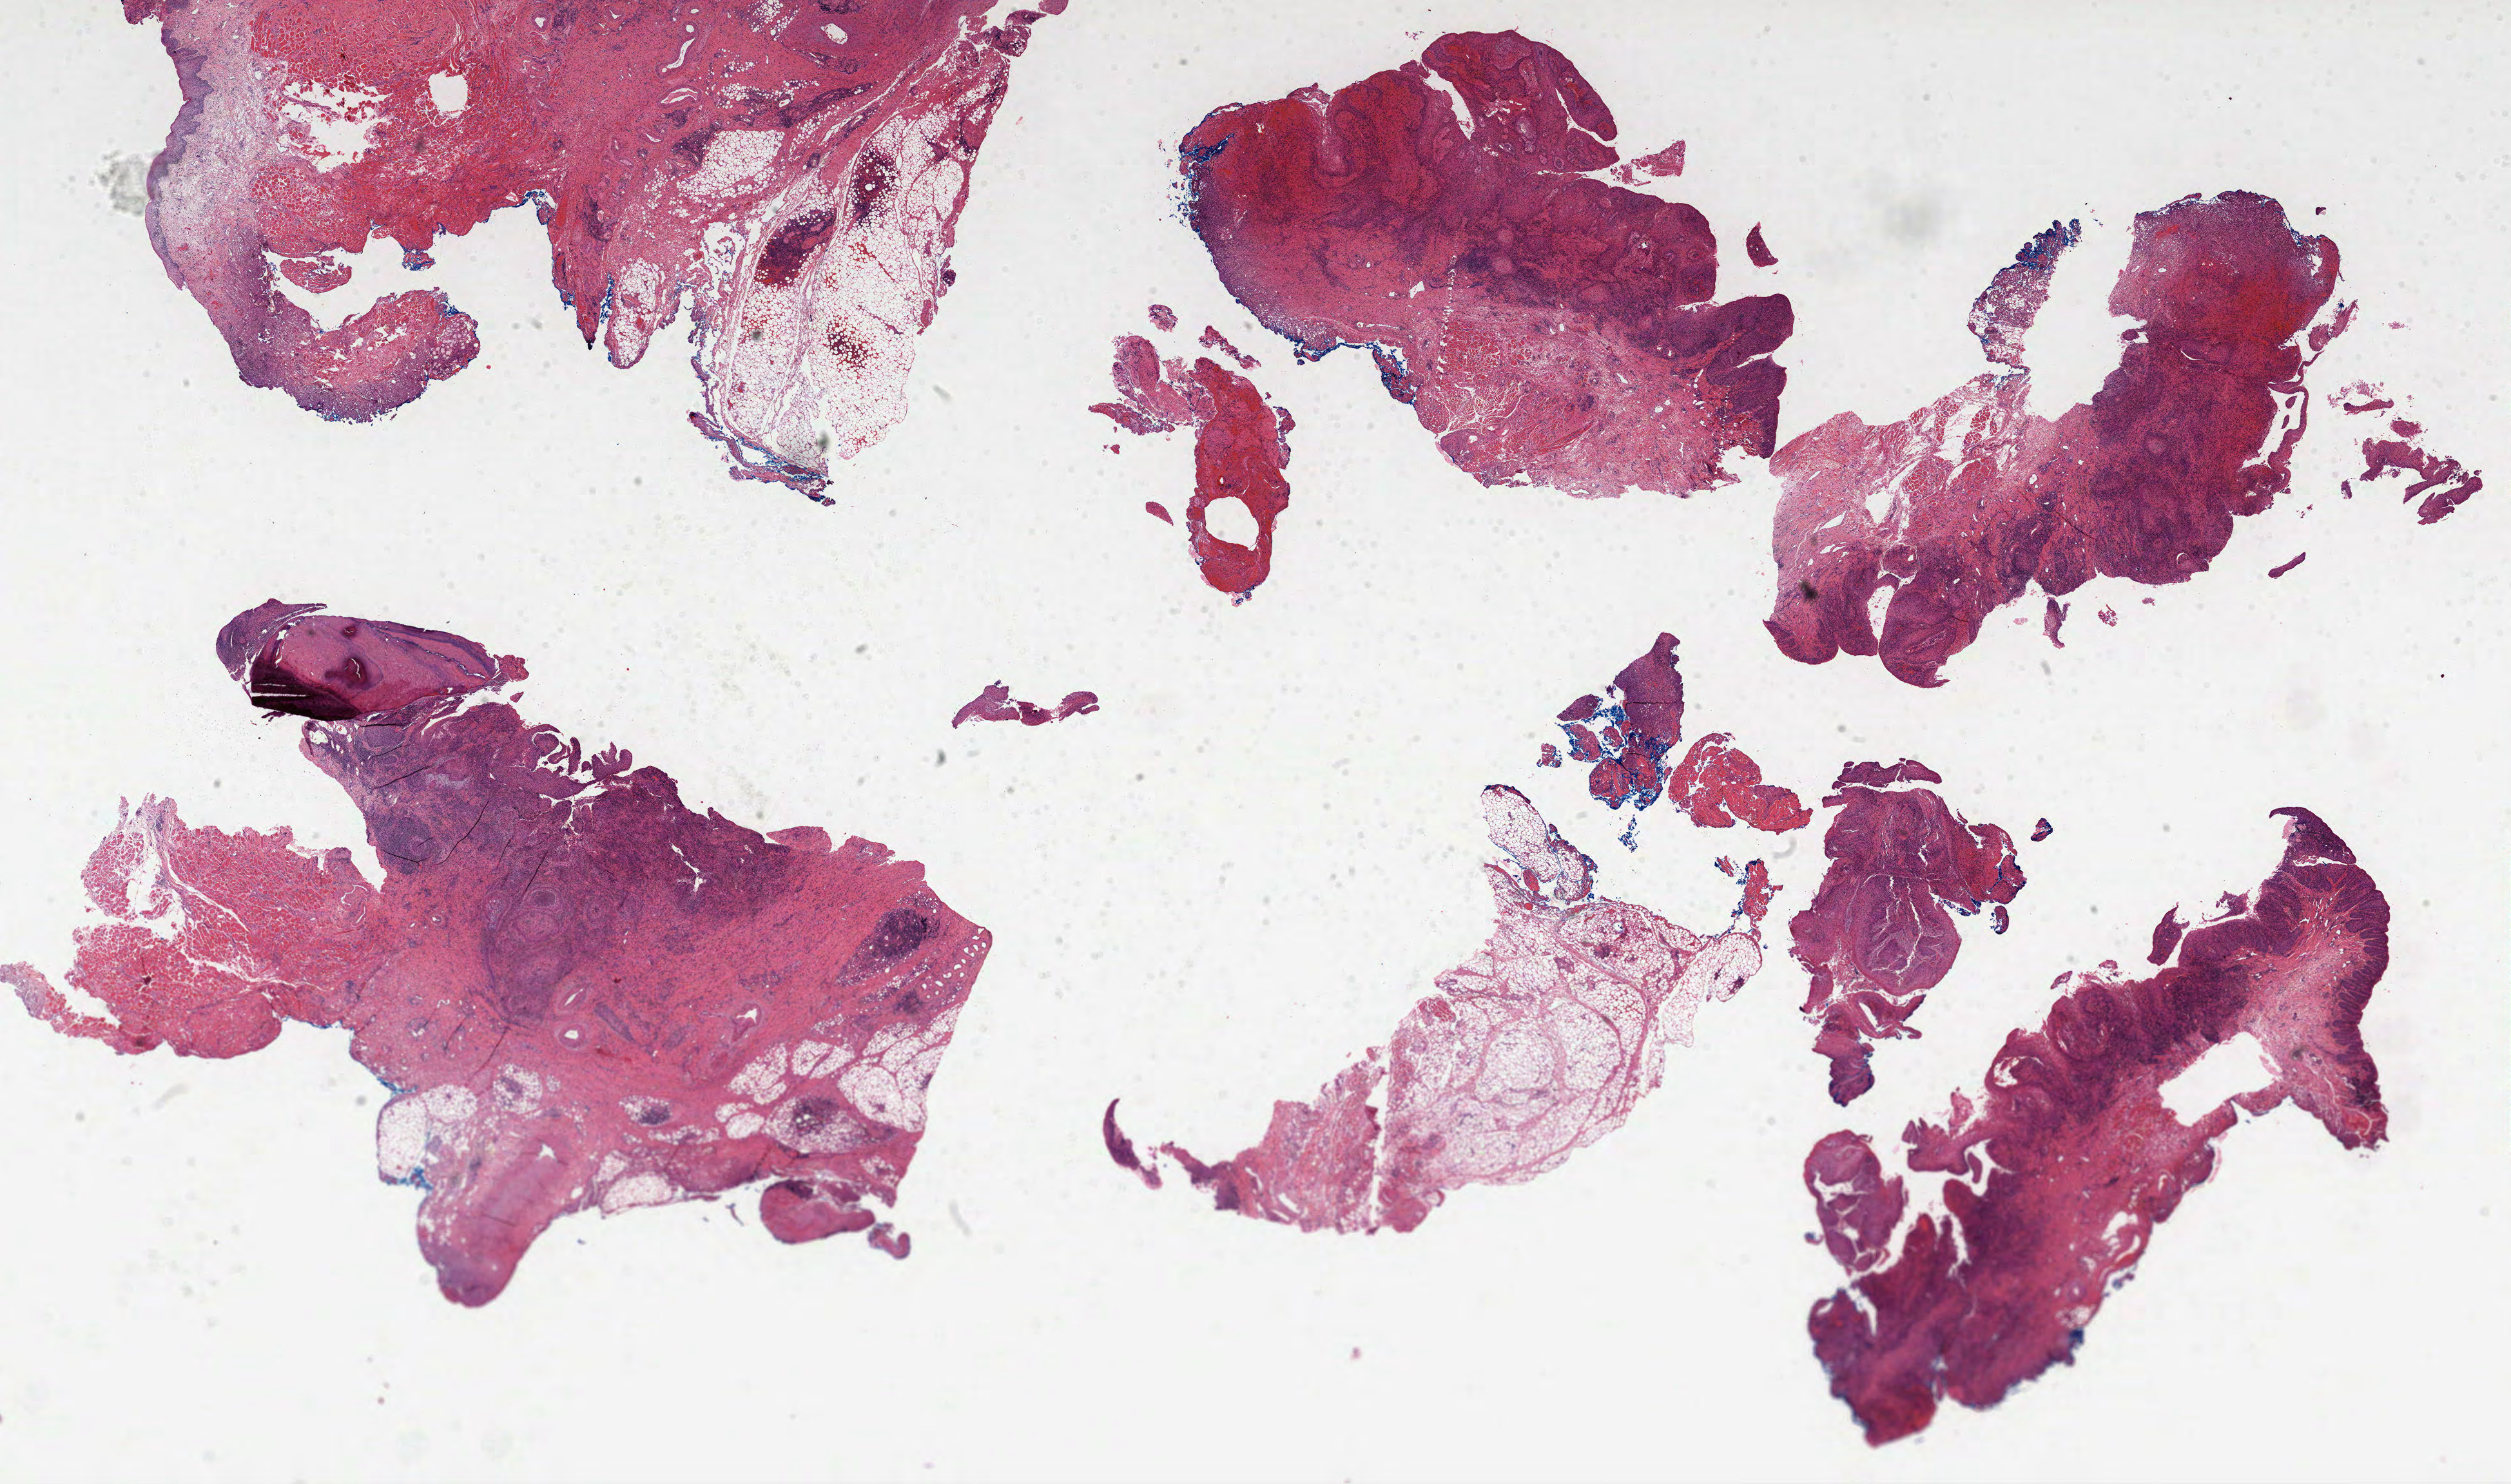
Digitized Hematoxylin and eosin (H&E) stained tissue section (whole slide), low-resolution overview of the scanned area, about 31.4 x 18.6 mm (acquisition: 40x scan), FFPE section, head and neck, primary tumour sample. Patient sex: female. Histologic grade: G3 (poorly differentiated).
AJCC pathologic stage: IVA (6th edition). Histologic diagnosis: Squamous cell carcinoma, NOS (hard palate). TNM: T4a N0 M0.